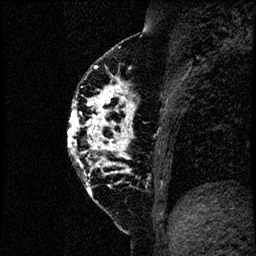
Breast MRI (dynamic contrast-enhanced), one sagittal slice. Position 32 of 60 along the scan axis. Dynamic contrast-enhanced study with each time point stored as its own series, time point 2 of 4 at this slice position (early post-contrast, ordered by acquisition time). 1.5 T. TE 4.2 ms, TR 17.6 ms. 2 mm slice thickness. 256 × 256 image matrix, field of view 200 × 200 mm. Patient: female, 40 years. Case-level facts recorded for this patient, not image findings: setting: breast cancer imaged before/during neoadjuvant chemotherapy; receptor status: HER2-positive.
Structures marked on this image (semi-automatic segmentation, software-assisted and operator-edited):
- analysis volume of interest (the breast-tissue region the enhancement analysis was run in; not a lesion): bounding box <66,55,185,206> (left, top, right, bottom; pixels)
- tumour enhancement mask (voxels above the 100 % enhancement threshold inside the analysis volume of interest): <67,66,133,175>